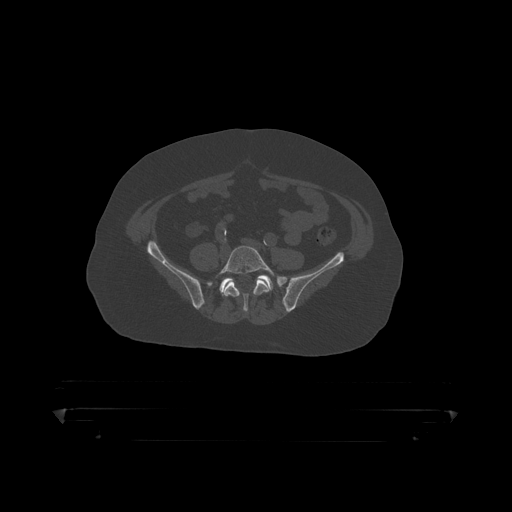
CT including the spine, one axial slice. Slice 36 of 390 in the series (ordered by position). Reconstruction kernel STANDARD. 120 kVp. Bone window (W 1800 / L 400 HU). 1.25 mm slice thickness. 512 × 512 image matrix. Male patient, age 60 years. From the clinical record (not read from this slice): primary cancer: prostate.
Outlined on this slice (semi-automatically segmented with operator editing):
- L5 vertebra: box from (x=215, y=246) to (x=280, y=313) px